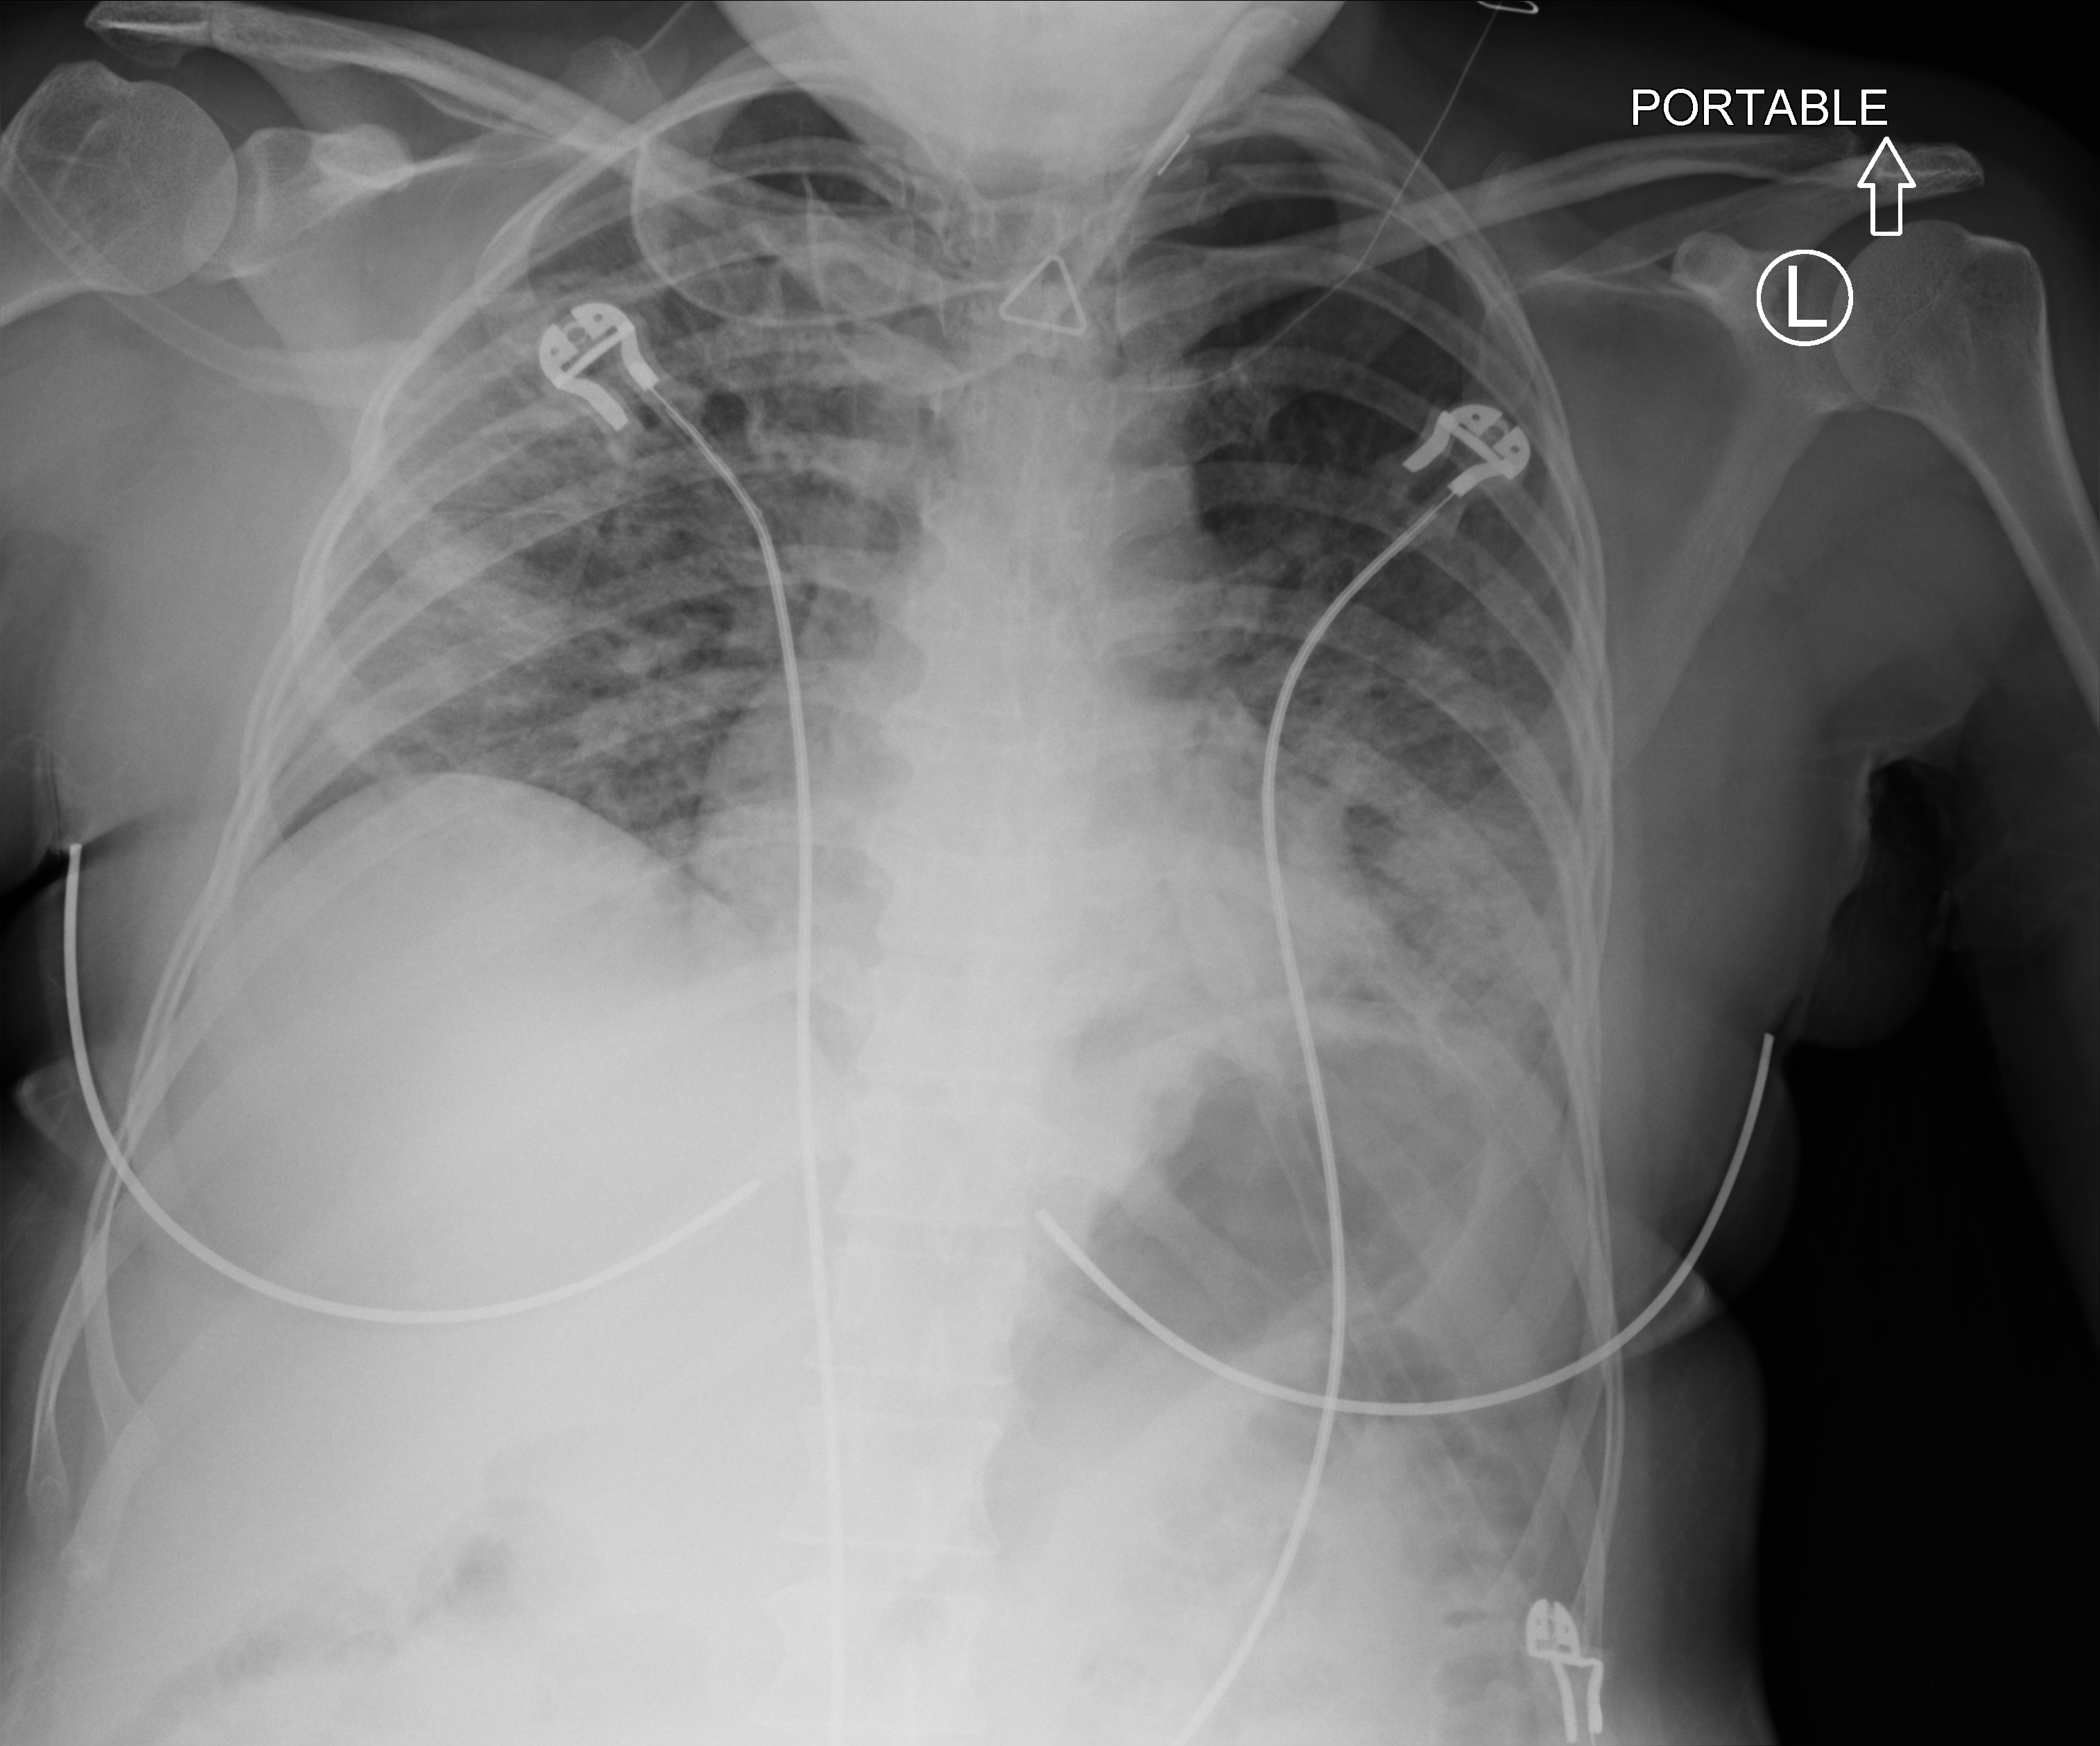
Portable chest radiograph. Patient hospitalised with COVID-19; female, aged 18–59 years.
From the hospital-stay record, not from the radiograph (when in the stay this image was taken is not recorded): chronic kidney disease (admission record): no.